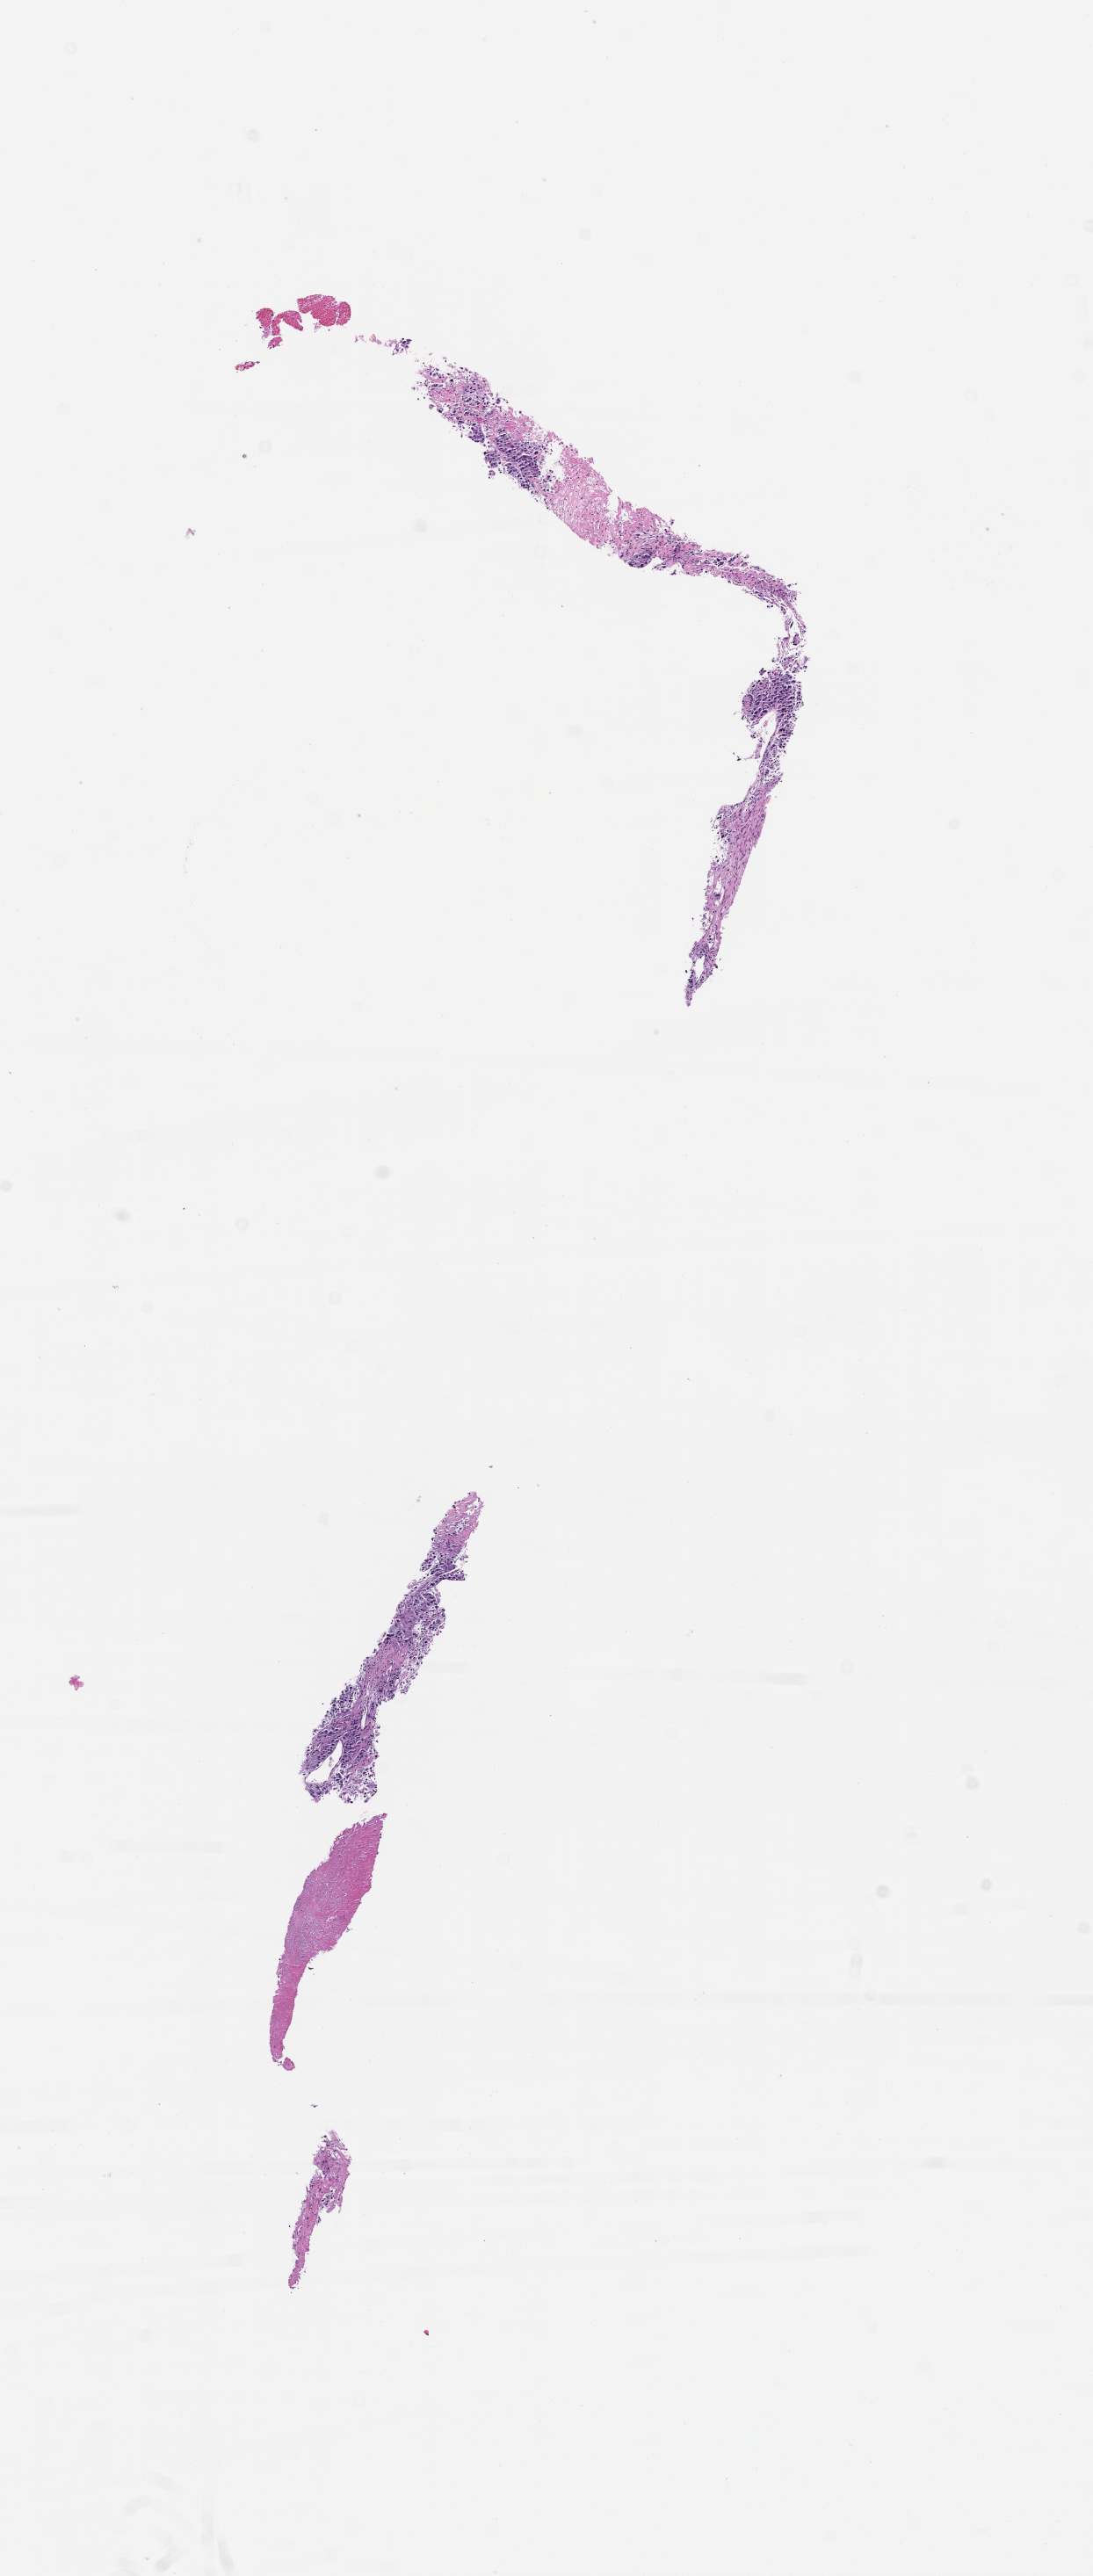
Whole-slide image, H&E stain, whole scanned area (about 5.0 x 11.8 mm) shown as a low-resolution overview. Formalin-fixed, paraffin-embedded (FFPE) tissue. Collected at baseline (before treatment). Male patient.
- this section: metastatic tumor tissue
- patient diagnosis (primary): Non-Small Cell Lung Carcinoma